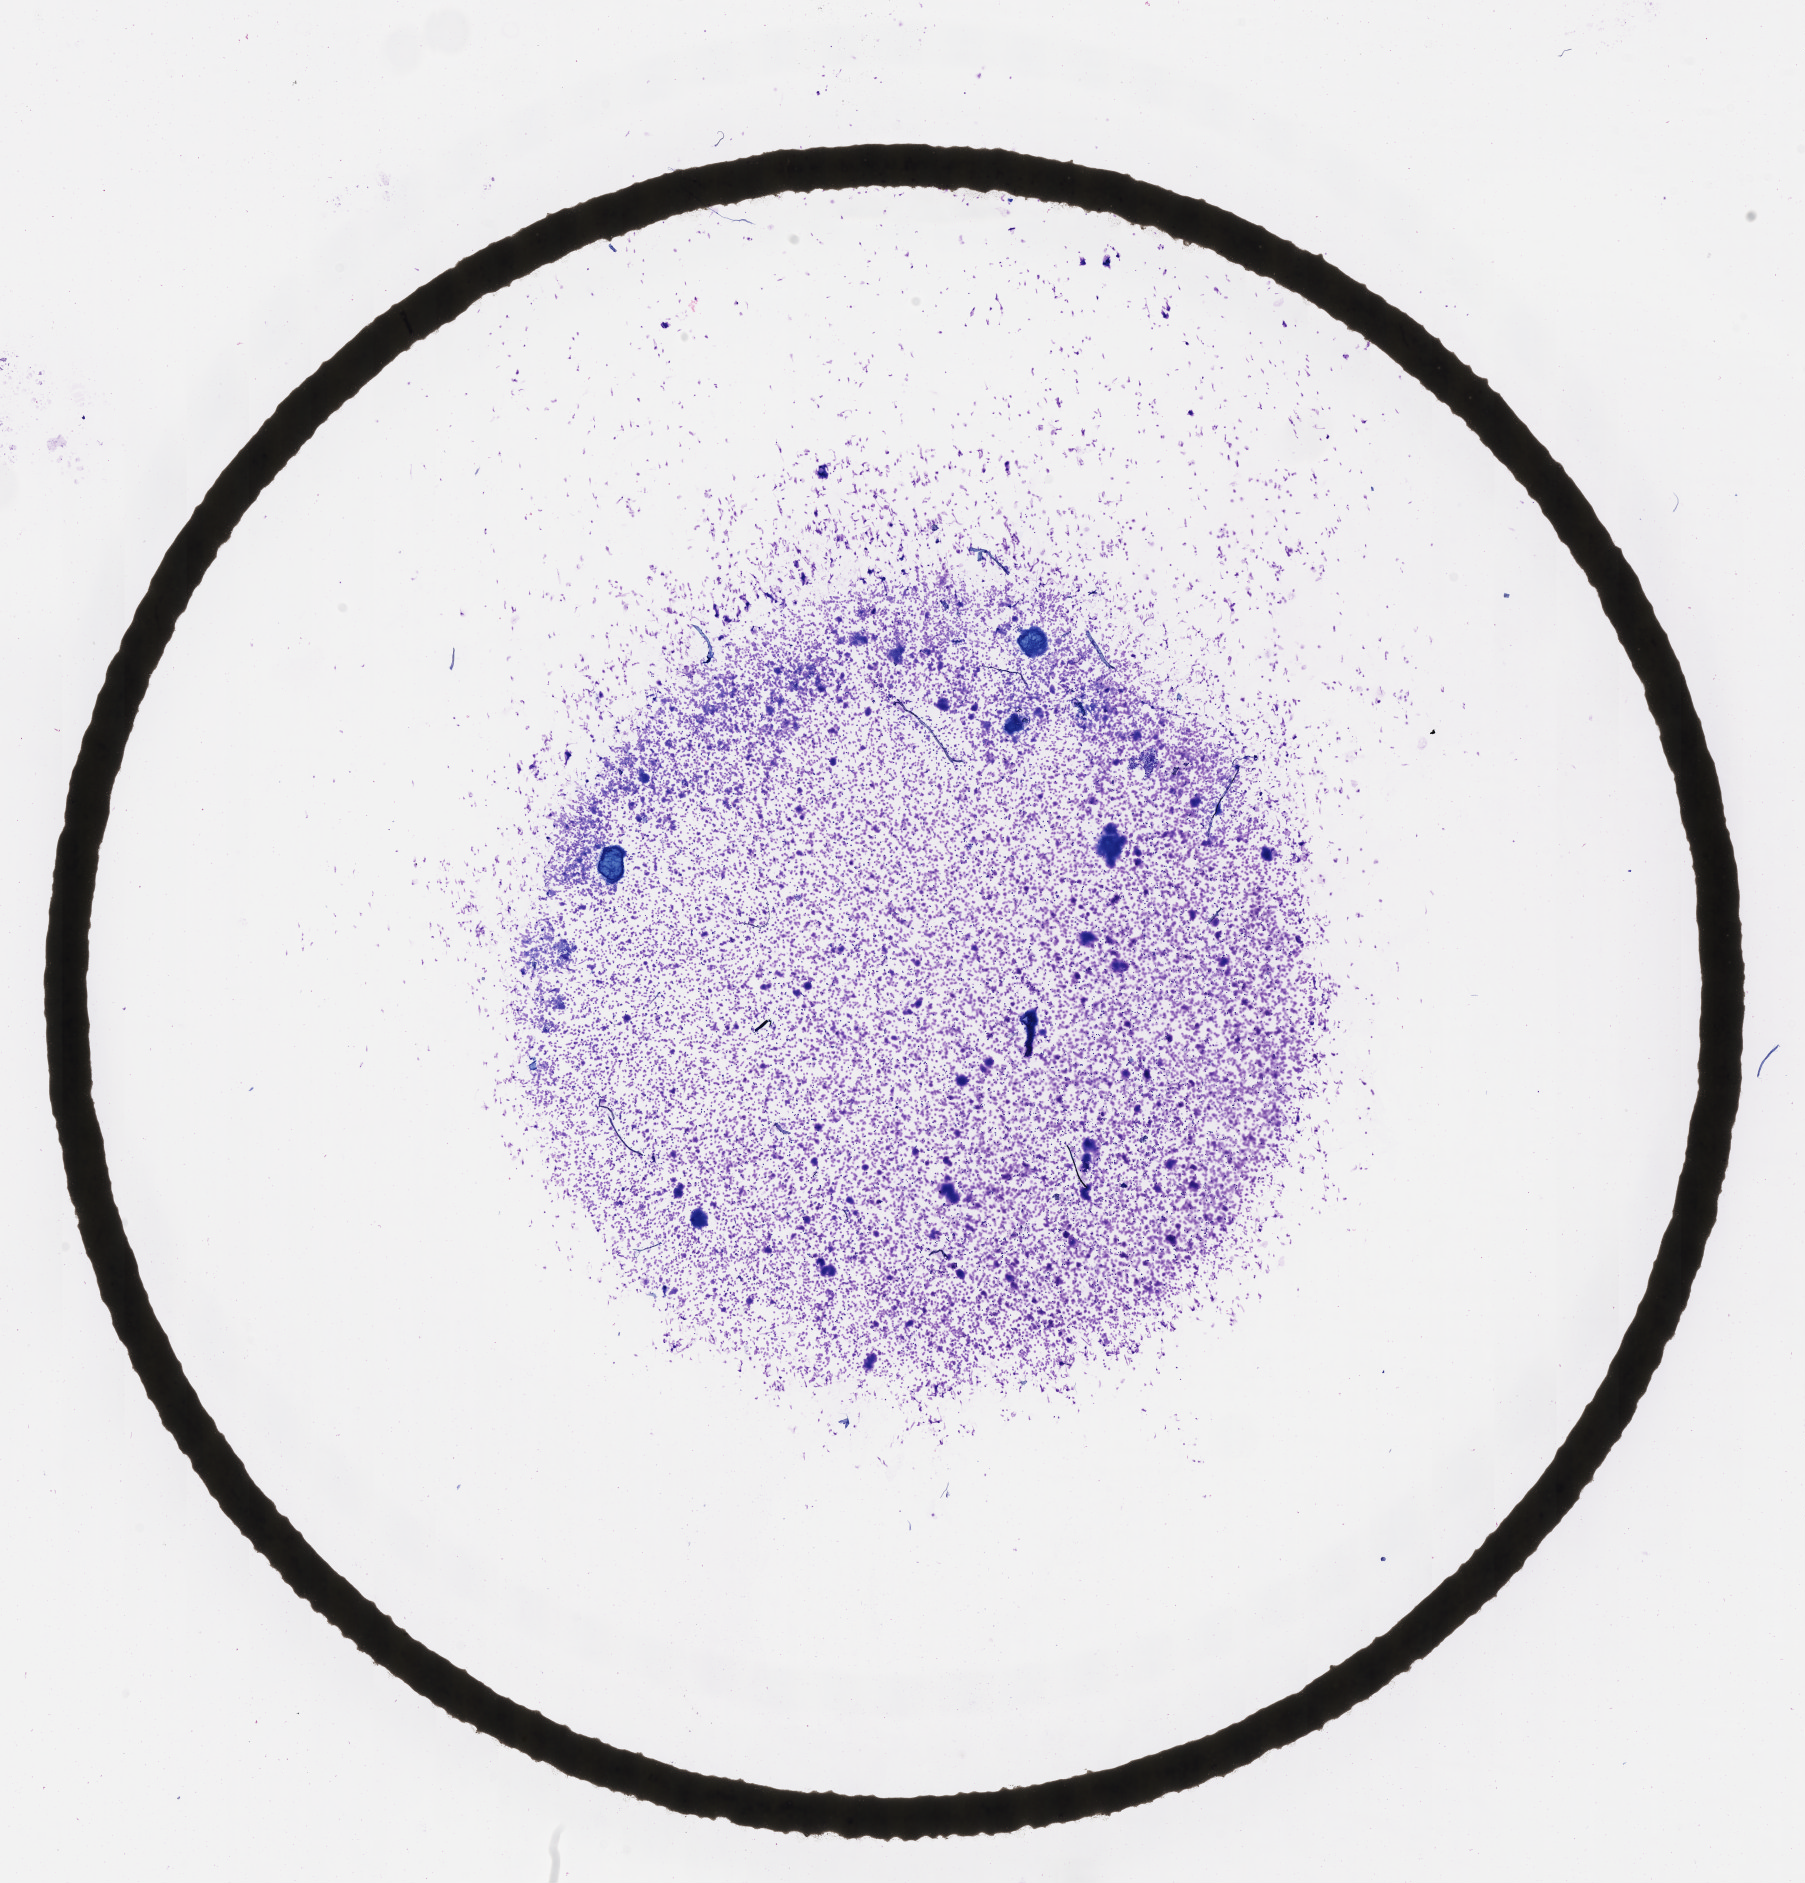
Whole-slide image, Wright–Giemsa stain, low-resolution overview of the scanned area, about 14.6 x 15.2 mm; cryosection; primary tumor; anatomic site: lymph node of head and neck. Male, age 3 years at initial diagnosis. Pathologist review of this section (percent, as recorded): tumor cells 90%, tumor nuclei 90%, stromal cells 5%, necrosis 0%, normal cells 5%. Infiltration values recorded for this section: lymphocyte infiltration 65%, monocyte infiltration 20%, neutrophil infiltration 10%.
• section: top of the tissue portion
• diagnosis: Burkitt lymphoma, NOS
• Ann Arbor stage (patient): Stage III